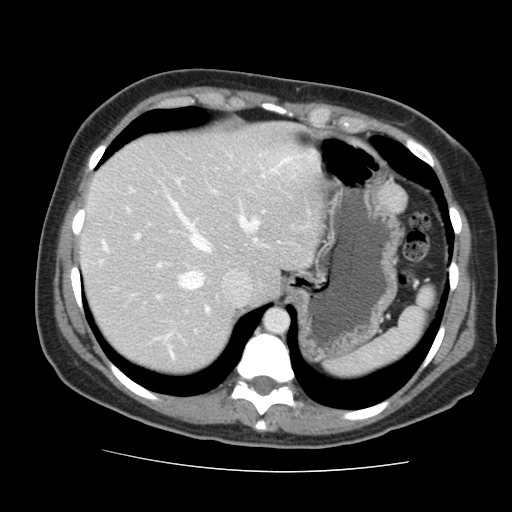
Contrast-enhanced abdominal CT, one axial slice. Intravenous contrast given. Soft-tissue window (W 400 / L 40 HU). 2.5 mm slice thickness. 512 × 512 image matrix. Female patient, age 46 years. From the clinical record (not read from this slice): diagnosis: colorectal cancer liver metastases, imaged before liver resection; multiple liver metastases: no; largest metastasis: 2.8 cm; disease in both lobes: no.
Structures marked on this image (expert manual segmentation):
- hepatic veins: bounding box (x1, y1, x2, y2) in pixels: (103, 200, 311, 340)
- liver: (82, 127, 322, 372)
- planned liver remnant (the part of the liver to remain after resection): (82, 127, 322, 372)
- portal vein (with intrahepatic branches): (127, 180, 215, 357)